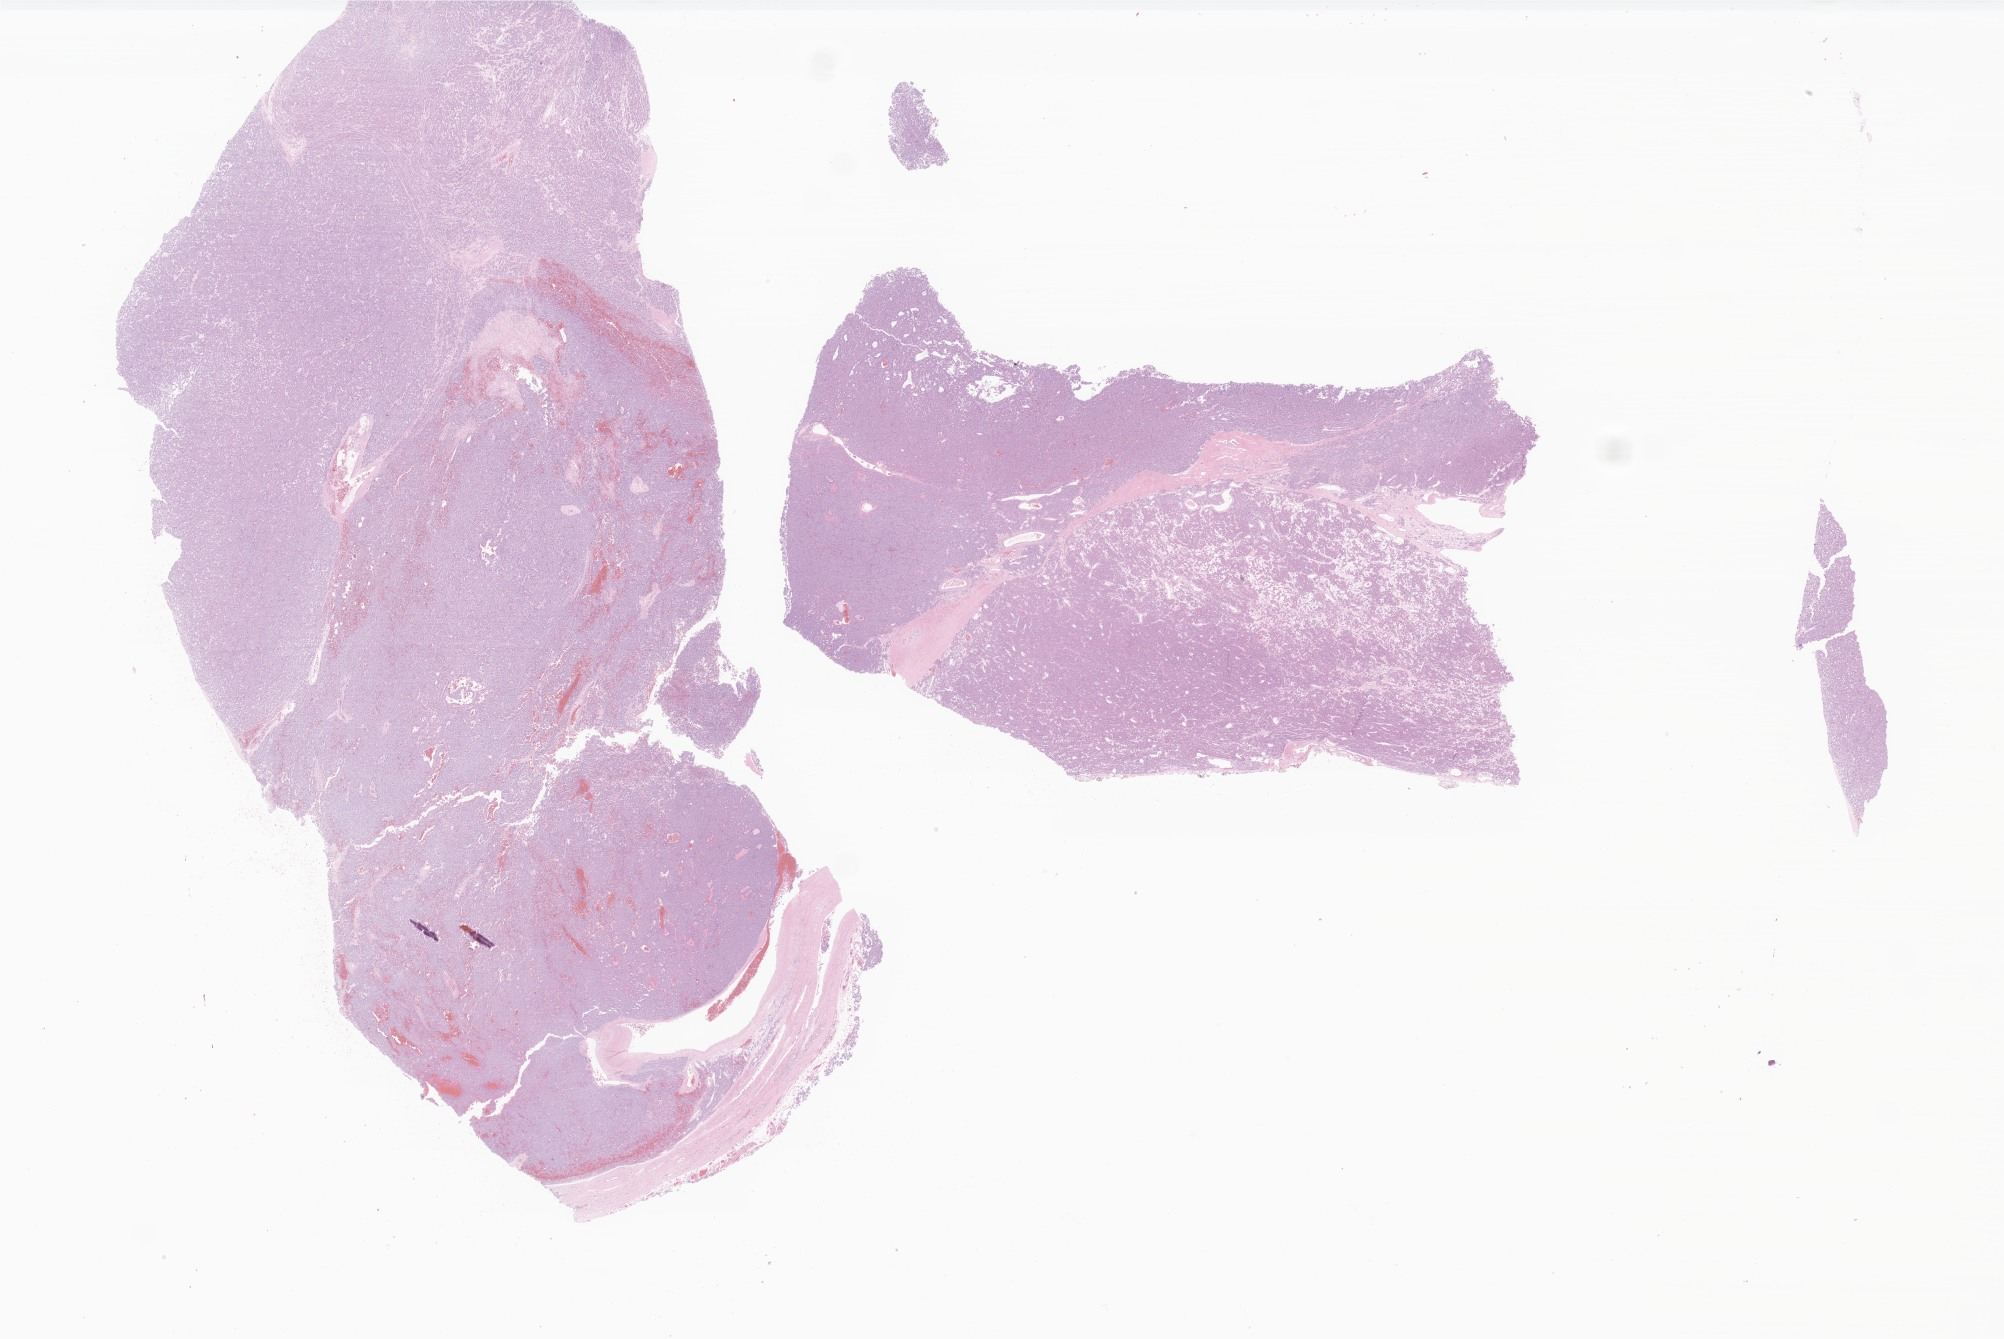
Whole-slide image, hematoxylin and eosin (H&E) stain of tumor tissue from the peritoneum, a low-resolution overview of the entire scanned area, about 33.8 x 22.6 mm; FFPE section. Patient female; age 91 months (7 years 7 months).
Diagnosis: Pancreatoblastoma.